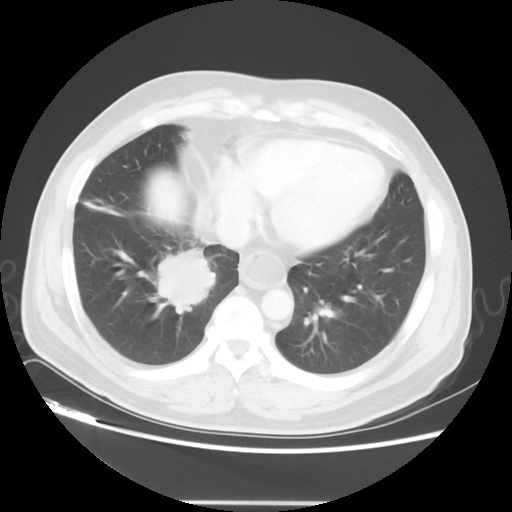
Chest CT, one axial slice; reconstruction kernel STANDARD; 120 kVp; lung window (W 1500 / L -600 HU); 5 mm slice thickness; 512 × 512 image matrix, field of view 390 × 390 mm. Male patient, age 53 years. Case-level facts recorded for this patient, not image findings: clinical TNM (as recorded): T2 N3 M0.
Outlined on this slice (bounding box drawn by a radiologist):
- lung tumour (recorded histology: small cell carcinoma): bounding box (x1, y1, x2, y2) in pixels: (149, 241, 211, 314)